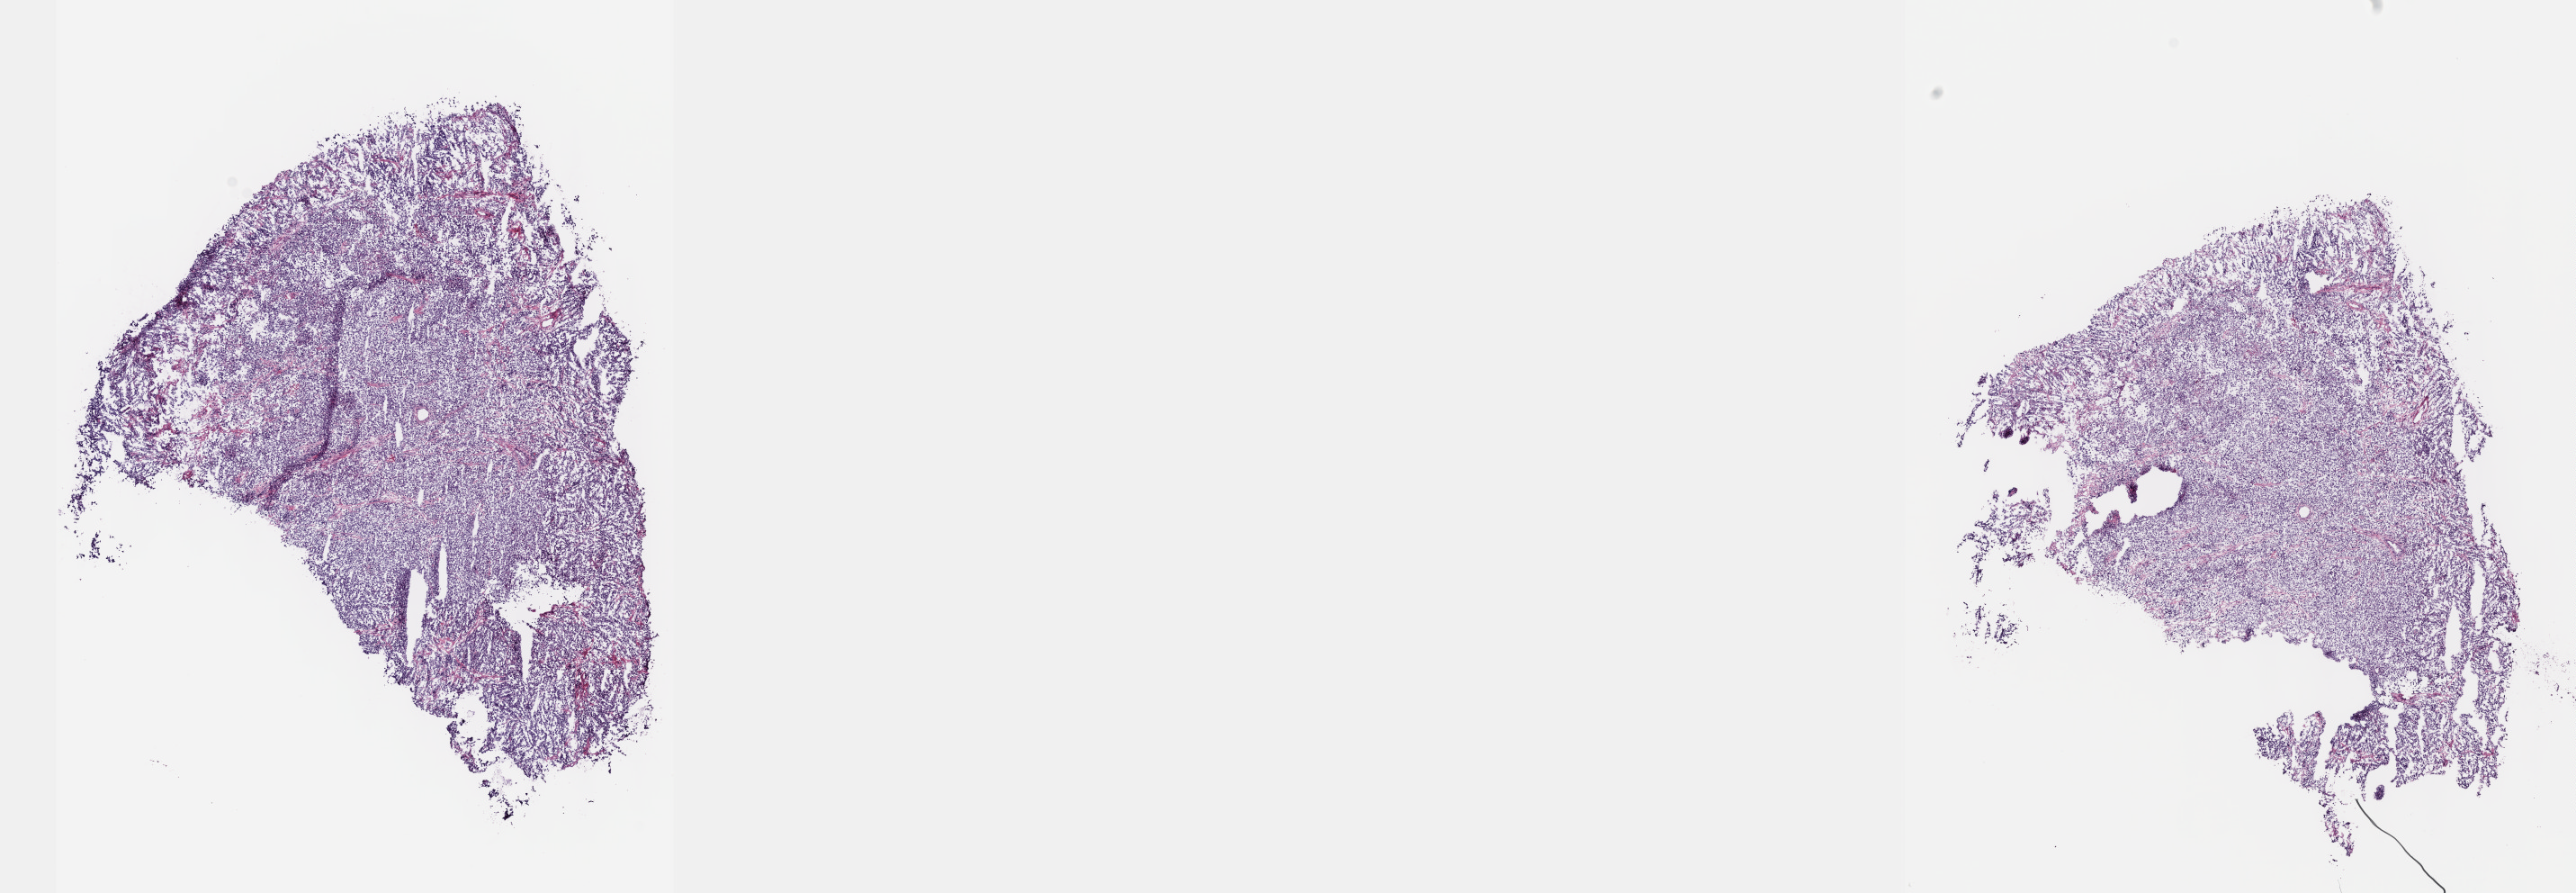
H&E-stained whole-slide image — a low-resolution overview of the entire scanned area, about 23.1 x 8.0 mm; frozen section from the top of the tissue portion; primary tumour sample from the testis. Patient: male, age at initial diagnosis 26 years. Composition of this section per pathologist review: tumour cells 100%, tumour nuclei 80%, normal cells 0%, stromal cells 0%, necrosis 0%. Inflammatory infiltration, as recorded: lymphocyte infiltration 1%, monocyte infiltration 0%, neutrophil infiltration 0%.
• diagnosis: Mixed germ cell tumor